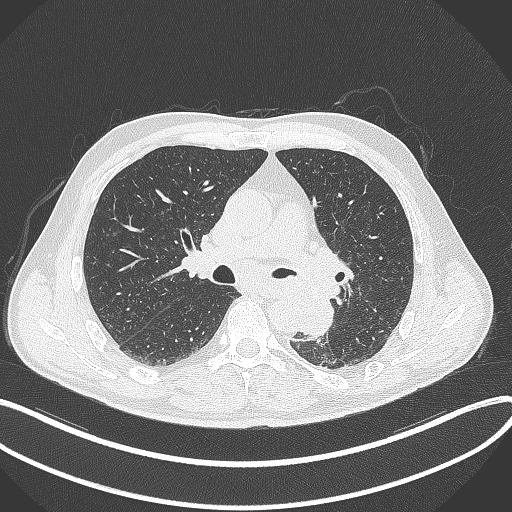
Chest CT, one axial slice. Slice 203 of 329 in the series (ordered by position). Reconstruction kernel B70f. 120 kVp. Lung window (W 1500 / L -600 HU). 1 mm slice thickness. 512 × 512 image matrix, field of view 400 × 400 mm. Patient: male, 59 years. From the clinical record (not read from this slice): clinical TNM (as recorded): T2a N2 M0.
Outlined on this slice (bounding box drawn by a radiologist):
- lung tumour (recorded histology: squamous cell carcinoma): bounding box [x1, y1, x2, y2] px = [293, 285, 335, 340]